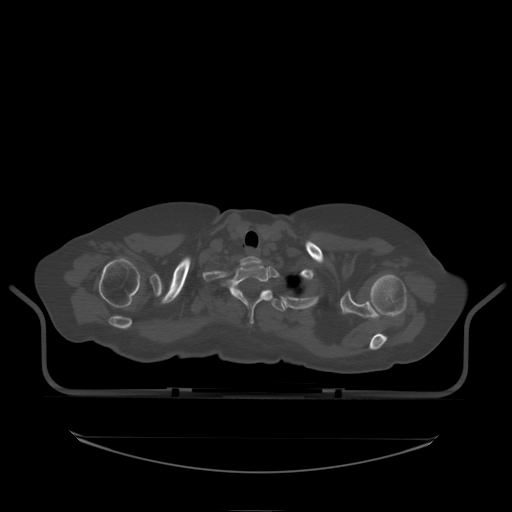
CT including the spine, one axial slice; slice 185 of 242 in the series (ordered by position); bone window (W 1800 / L 400 HU); 2.5 mm slice thickness; 512 × 512 image matrix. Patient: female, 53 years. From the clinical record (not read from this slice): primary cancer: lung; vertebrae with lytic lesions (as recorded): T7, L1.
Outlined on this slice (semi-automatically segmented with operator editing):
- T1 vertebra: box from (x=223, y=266) to (x=272, y=324) px
- T2 vertebra: (x=265, y=290)–(x=286, y=312)